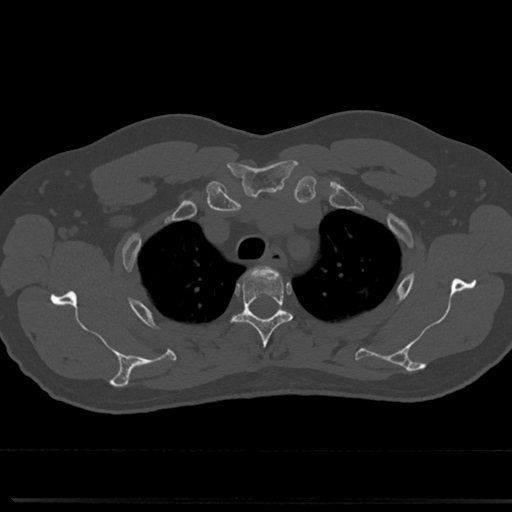
CT including the spine, one axial slice; position 591 of 817 along the scan axis; reconstruction kernel Br40s/3; 120 kVp; bone window (W 1800 / L 400 HU); 0.5 mm slice thickness; 512 × 512 image matrix. Male patient, age 61 years. From the clinical record (not read from this slice): primary cancer: prostate.
Annotated regions visible in this slice (semi-automatic segmentation, software-assisted and operator-edited):
- T3 vertebra: bounding box <235,266,292,365> (left, top, right, bottom; pixels)